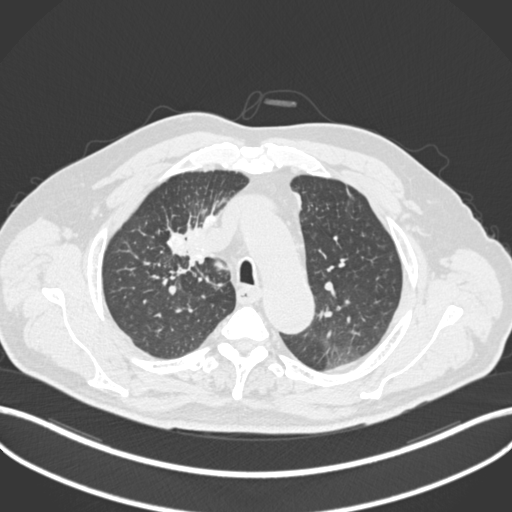
Chest CT, one axial slice; position 151 of 255 along the scan axis; 120 kVp; lung window (W 1500 / L -600 HU); 512 × 512 image matrix, field of view 400 × 400 mm. Patient: male, 60 years. From the clinical record (not read from this slice): clinical TNM (as recorded): T1b N1 M0.
Structures marked on this image (rectangle marked by the reading radiologist):
- lung tumour (recorded histology: squamous cell carcinoma): bounding box <163,218,209,275> (left, top, right, bottom; pixels)